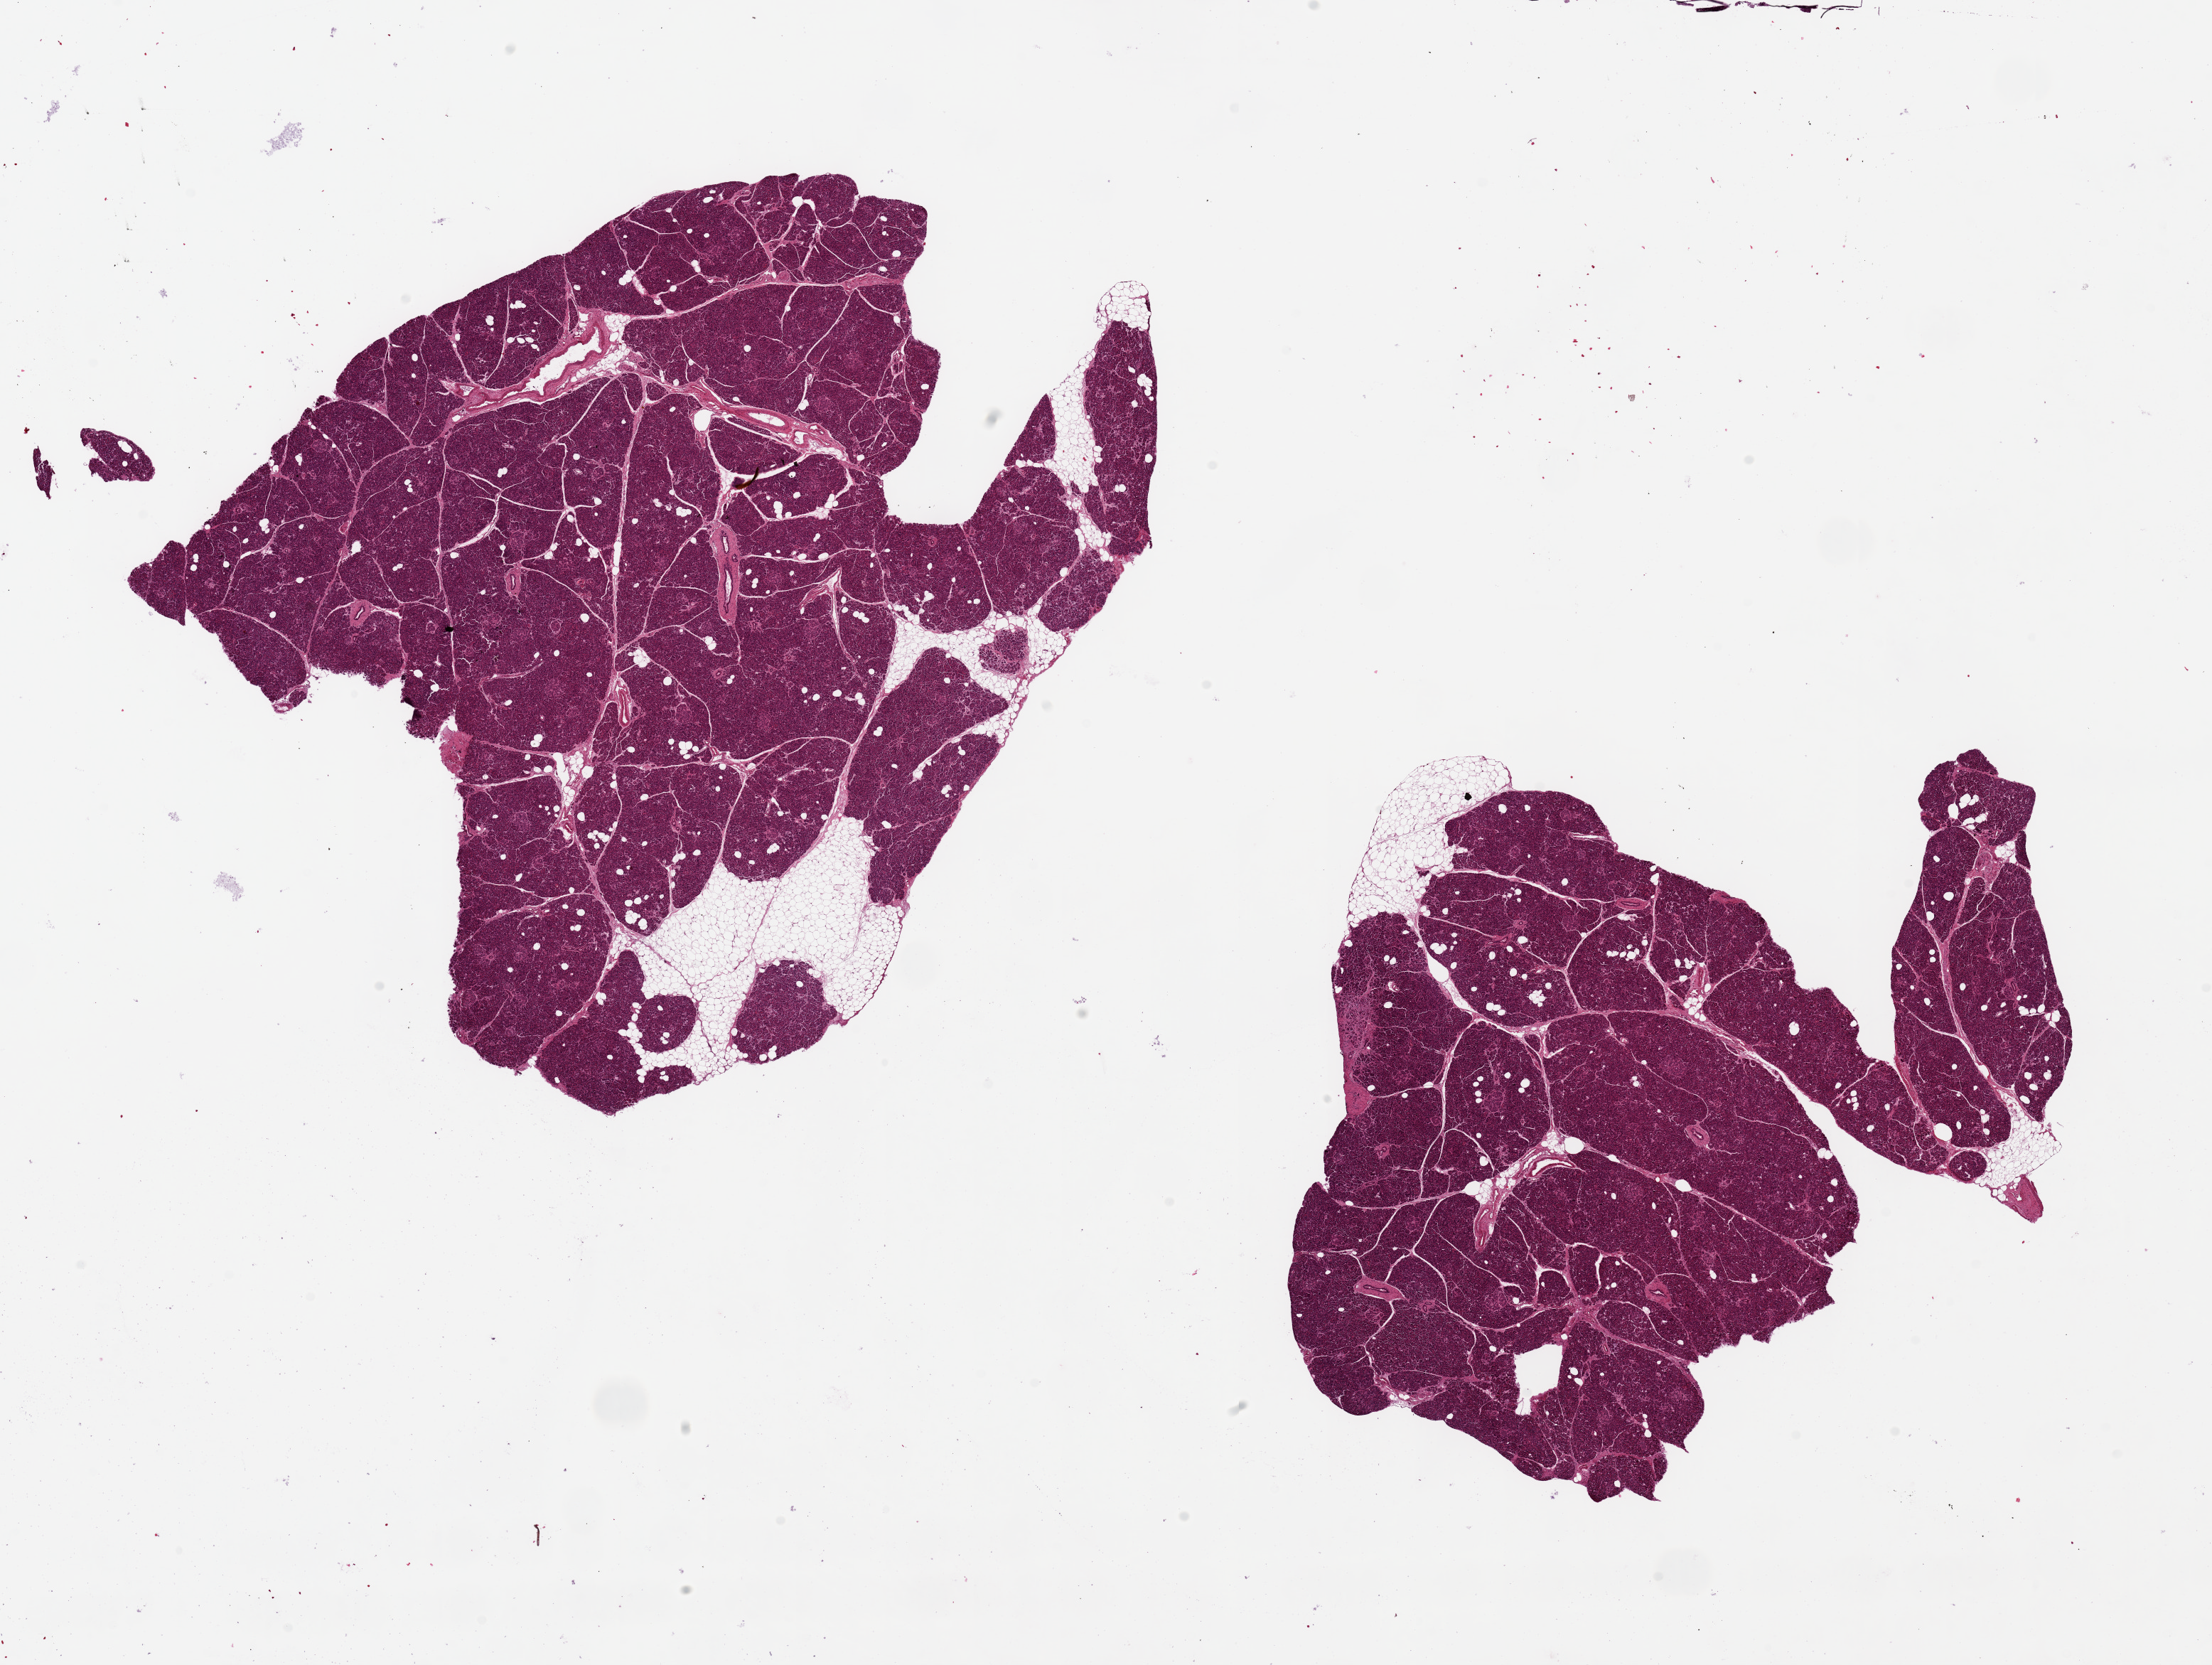
Digitized H&E-stained section, a low-resolution overview of the entire scanned area, about 24.6 x 18.5 mm (from a 20x scan), PAXgene-fixed paraffin-embedded (PFPE) section, section of pancreas (target tissue), donor tissue sample. Male donor.
Pathologist's review note for this sample: 2 pieces ~9x9mm, minimal fat, Islets well-visualized.